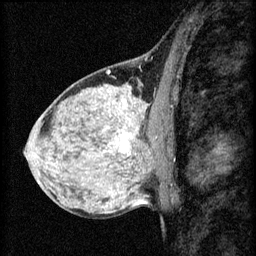
Breast MRI (dynamic contrast-enhanced), one sagittal slice. Slice 34 of 60 in the series (ordered by position). 3 images stored at this slice position (order not interpretable as contrast timing). 1.5 T. TE 4.2 ms, TR 8.2 ms. 2 mm slice thickness. 256 × 256 image matrix, field of view 180 × 180 mm. Patient: female, 40 years.
Outlined on this slice (semi-automatically segmented with operator editing):
- analysis volume of interest (the breast-tissue region the enhancement analysis was run in; not a lesion): bounding box (x1, y1, x2, y2) in pixels: (108, 108, 167, 159)
- tumour enhancement mask (voxels above the 70 % enhancement threshold inside the analysis volume of interest): (108, 108, 131, 155)